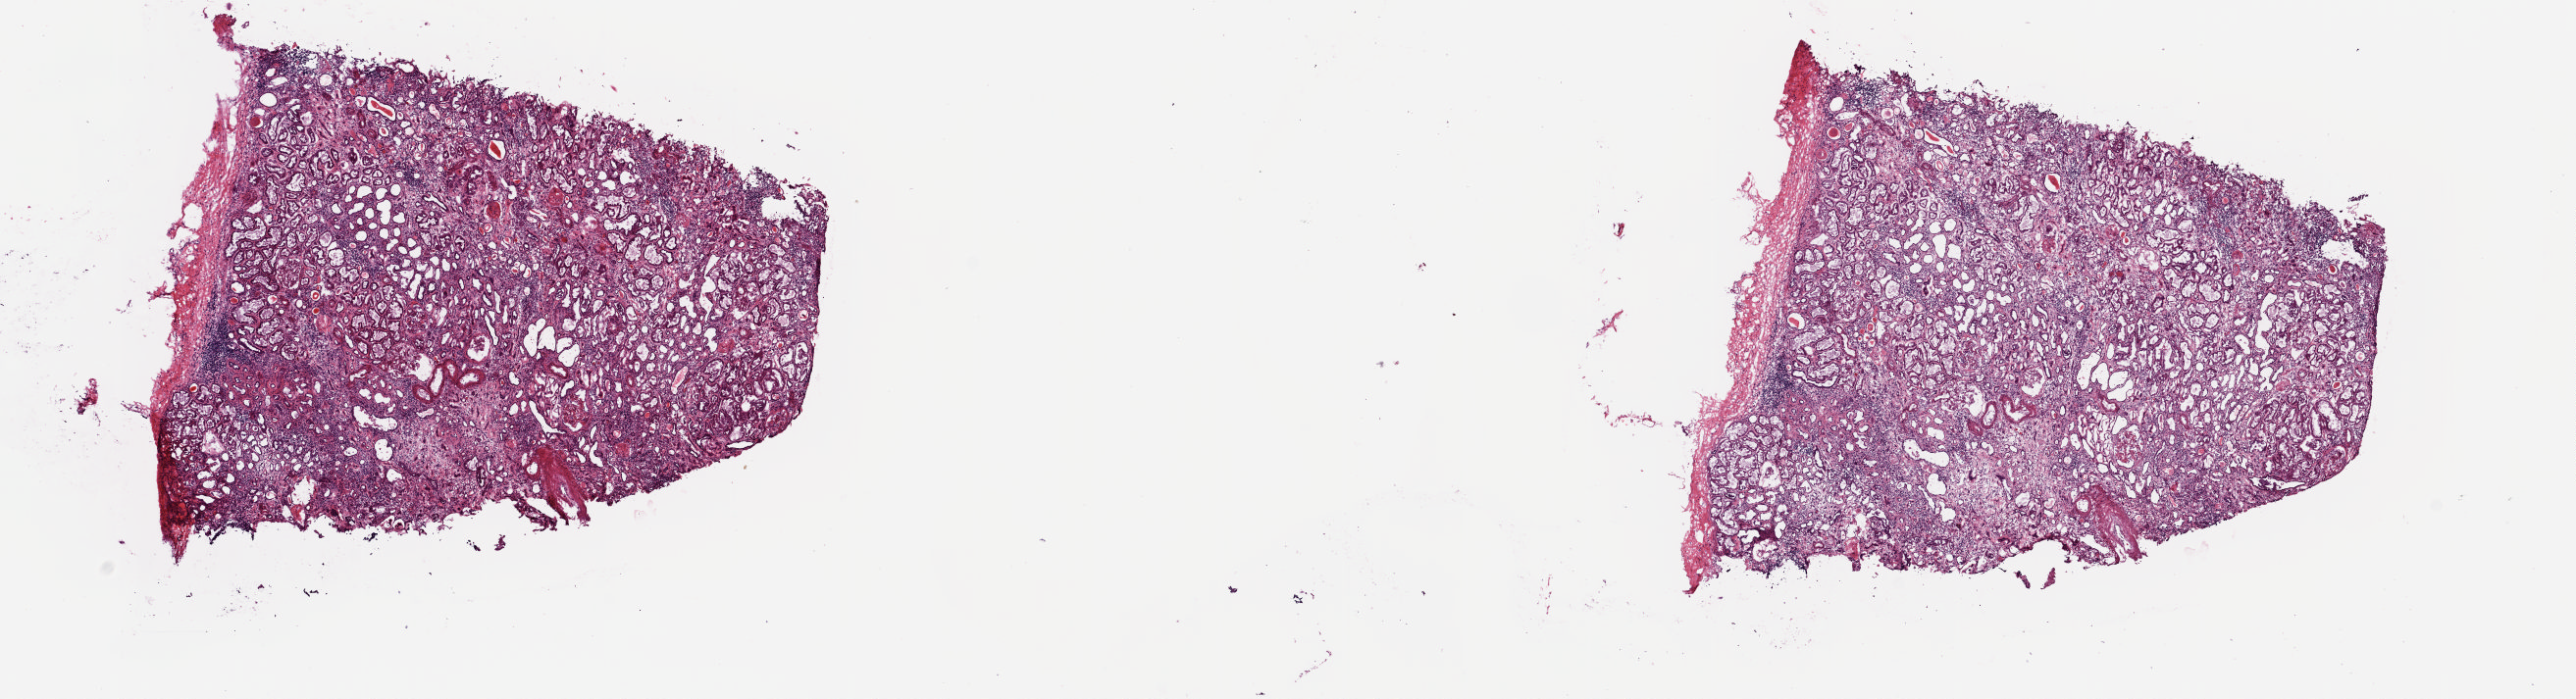
Whole-slide histology image, H&E-stained, low-resolution overview of the scanned area, about 20.8 x 5.7 mm (from a 20x scan). Frozen section from the top of the tissue portion. Solid tissue normal (non-tumour tissue) sample from the kidney. Patient: male, age at initial diagnosis 80 years. Slide review estimates, as recorded: tumour cells 0%, tumour nuclei 0%, normal cells 100%, stromal cells 0%, necrosis 0%. Inflammatory infiltration, as recorded: lymphocyte infiltration 15%, monocyte infiltration 1%, neutrophil infiltration 0%.
* this section: solid tissue normal (non-tumour) sample from the same patient
* patient diagnosis: Papillary adenocarcinoma, NOS